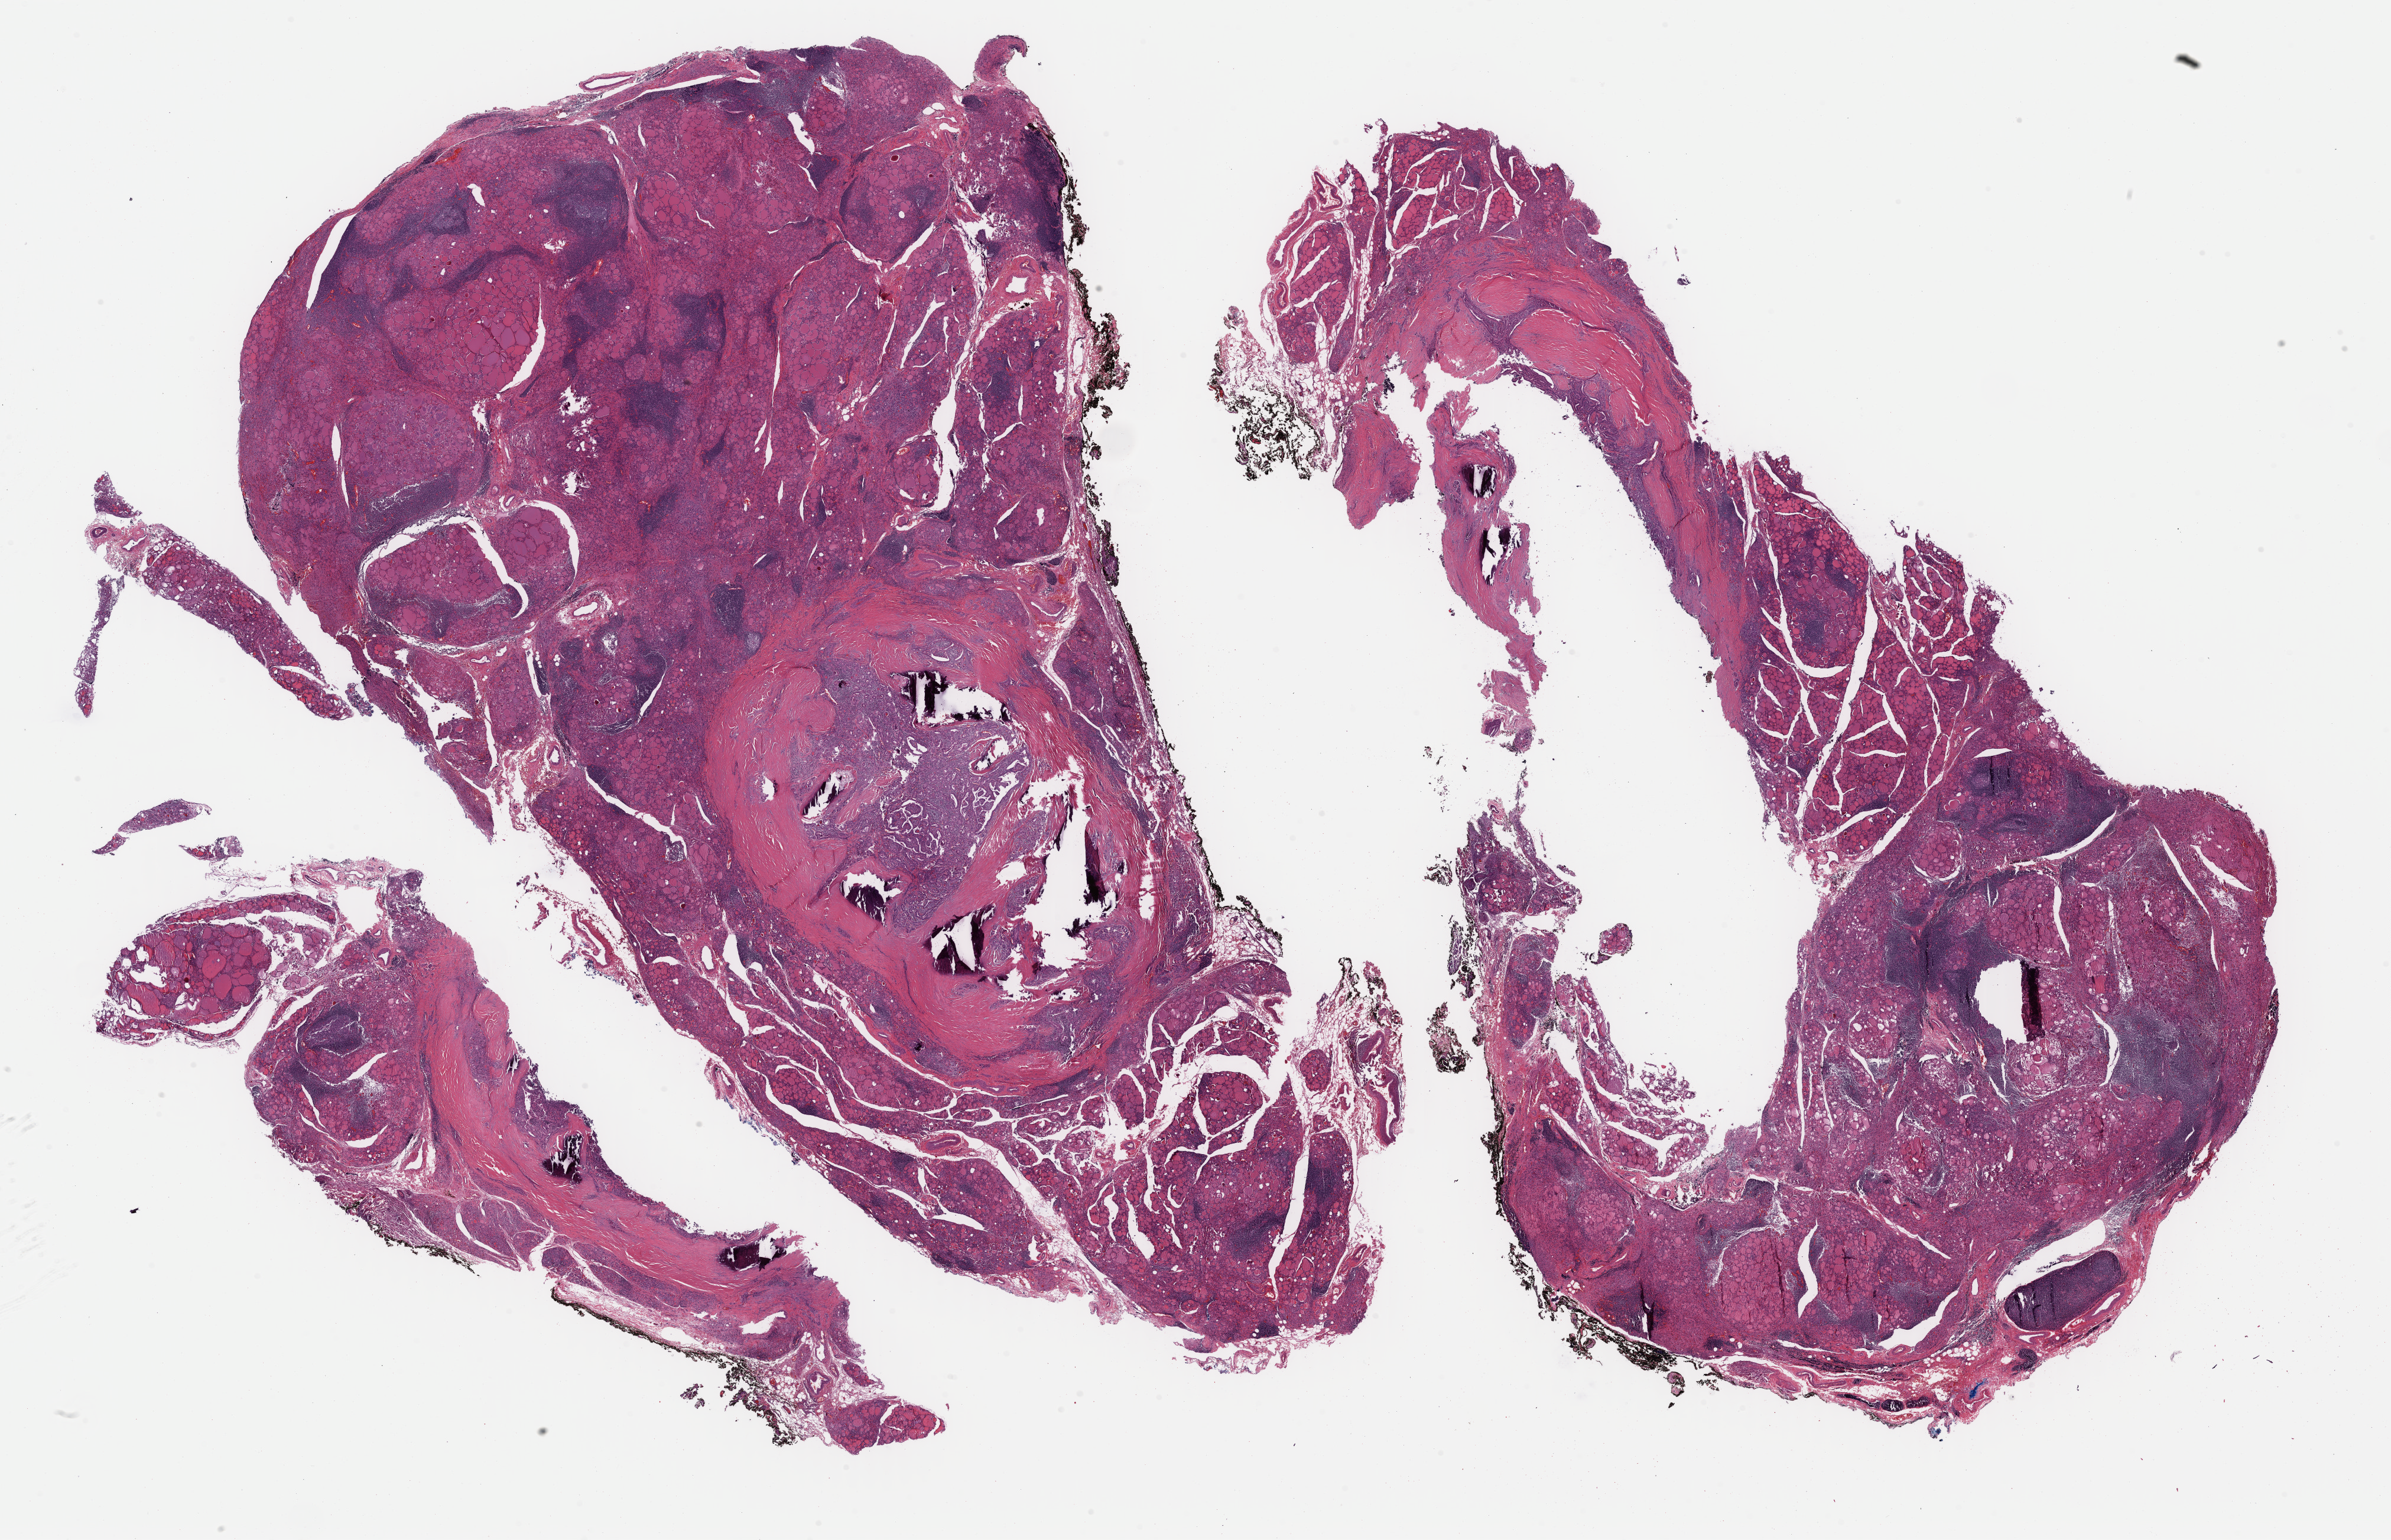
Digitized Hematoxylin and eosin (H&E) stained tissue section (whole slide) — shown as a low-resolution overview of the whole scanned area (about 31.9 x 20.6 mm, from a 40x scan), formalin-fixed paraffin-embedded (FFPE) diagnostic section, primary tumour sample from the thyroid. Female, age 50 years at initial diagnosis.
• lymph nodes positive (case pathology): 0 of 4 examined
• diagnosis: Papillary adenocarcinoma, NOS (thyroid gland)
• AJCC pathologic stage: I (6th edition)